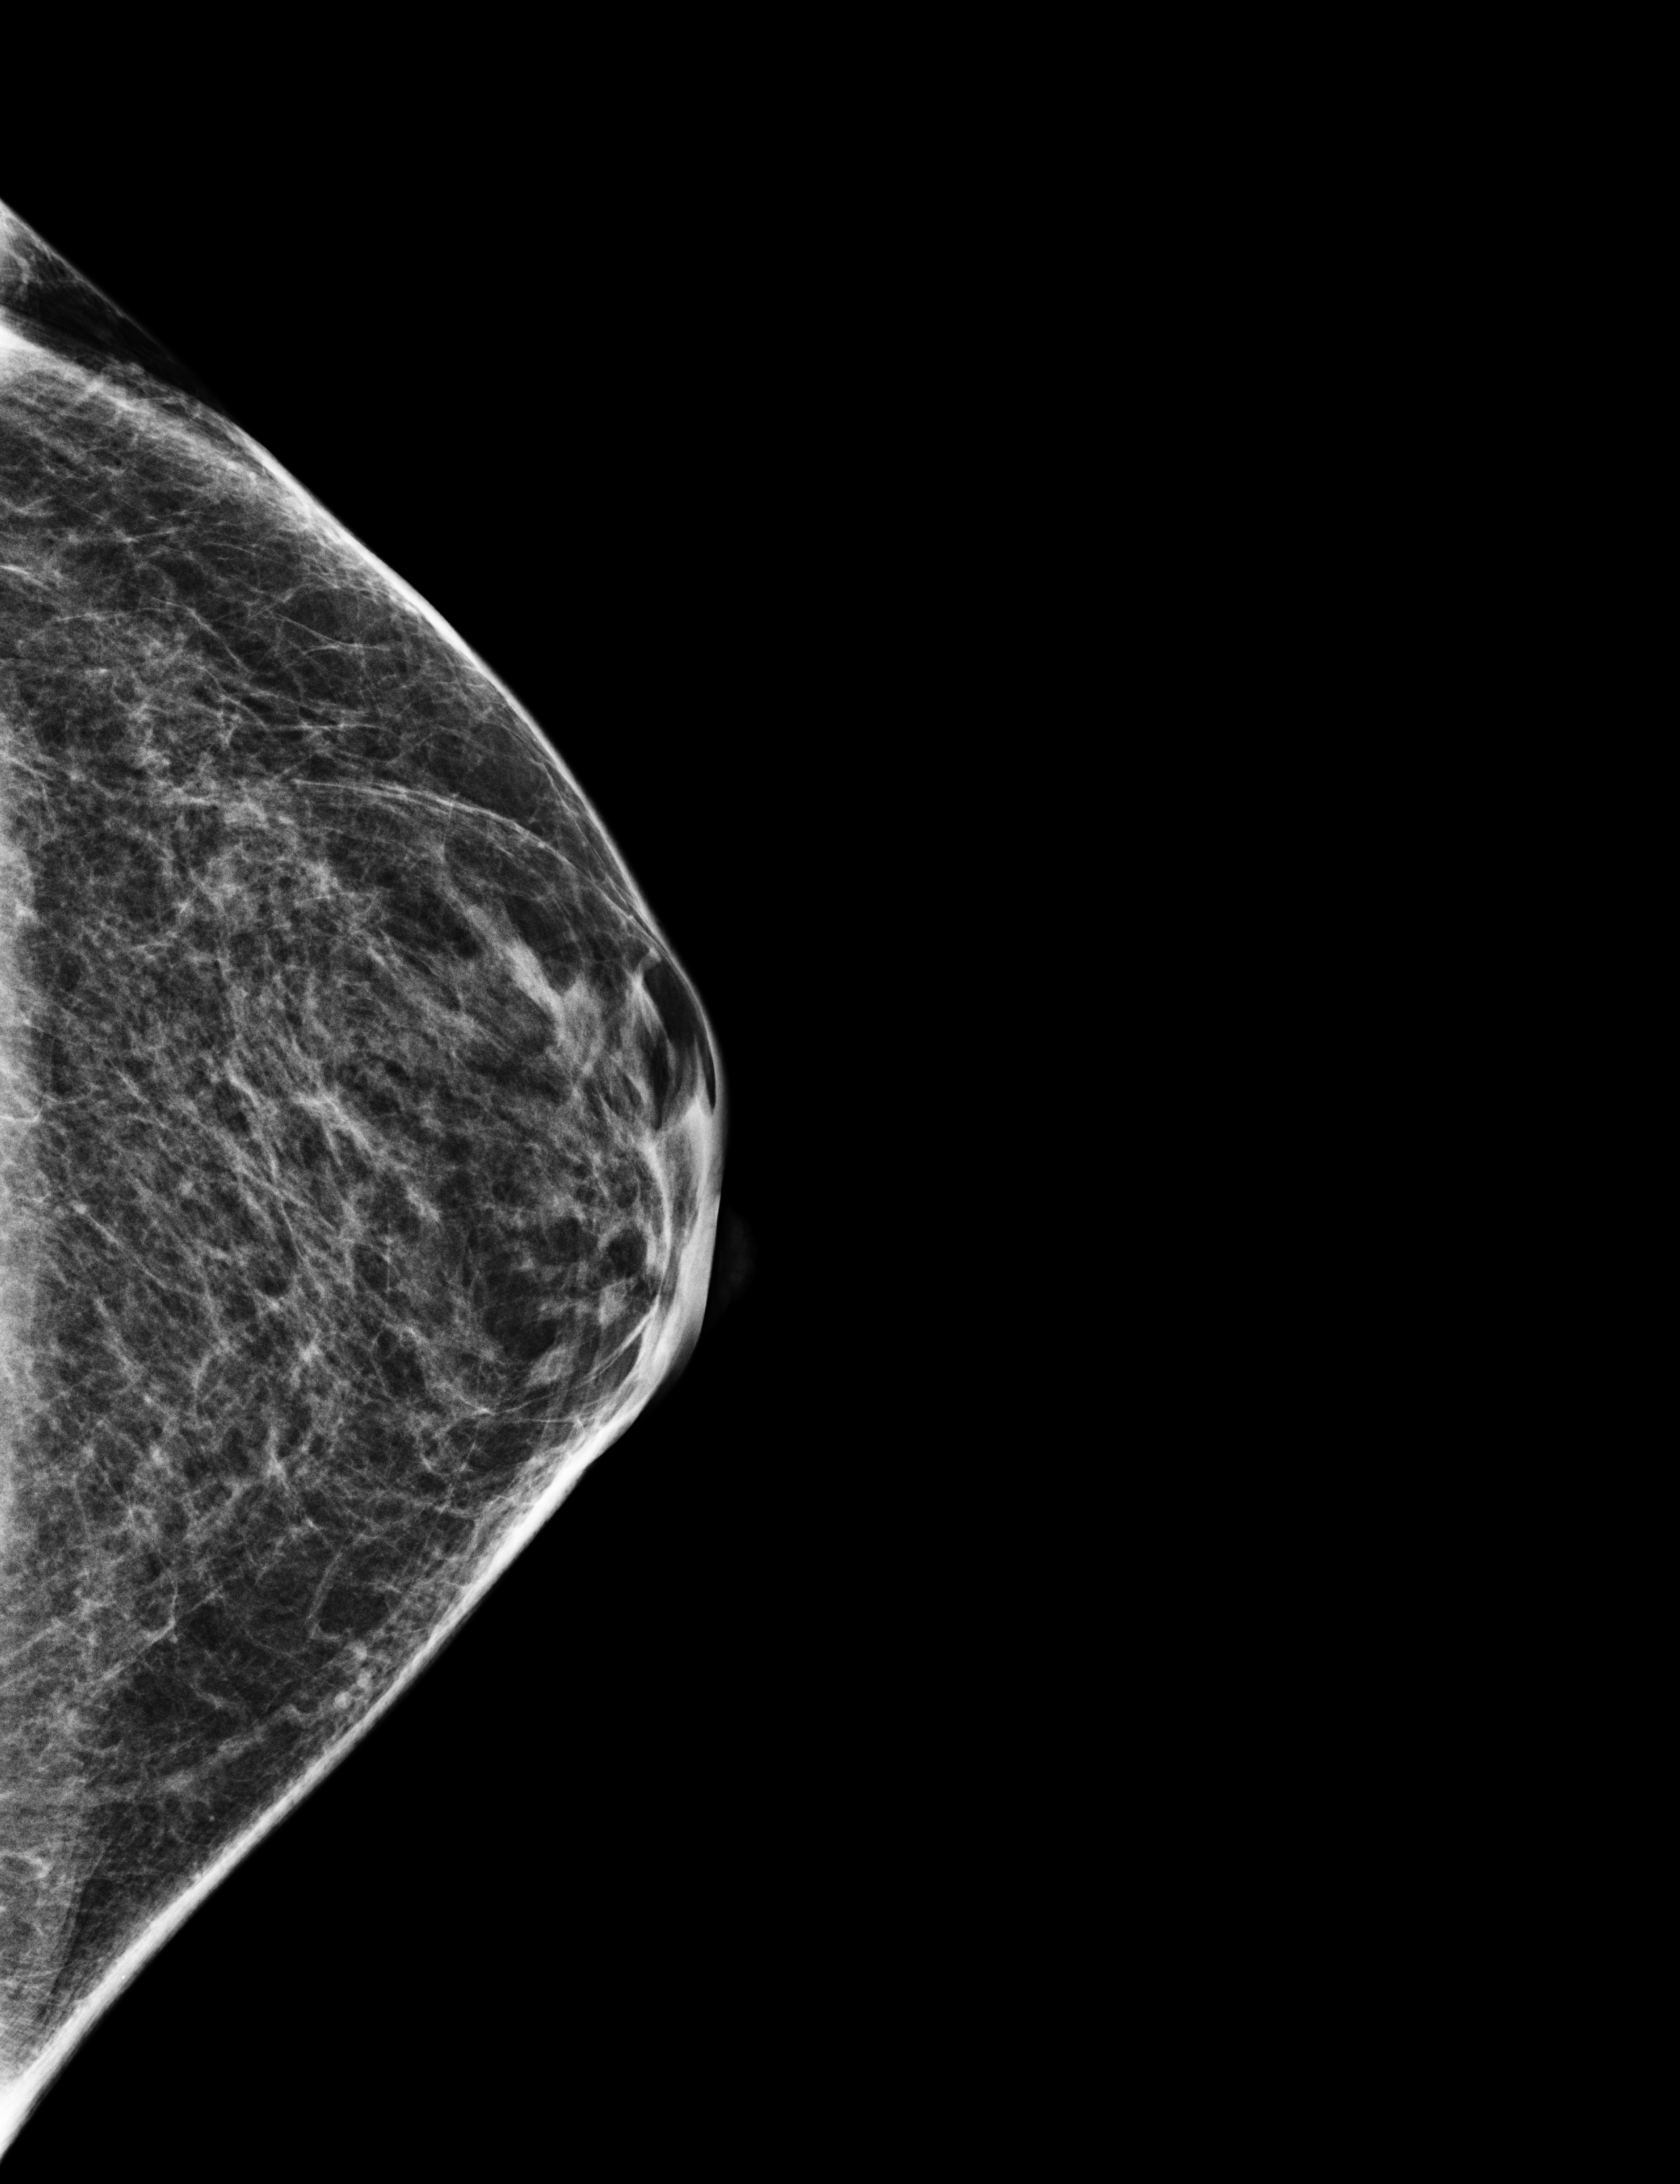
Digital mammogram (FFDM); left breast; craniocaudal (CC) view; screening examination. Female patient, age 51 years.
- BI-RADS breast density category at the screening exam (both breasts, scale 1–4): 3
- final BI-RADS assessment for this screening round (tomosynthesis exam, both breasts): category 2
- recall: no recall after this screen